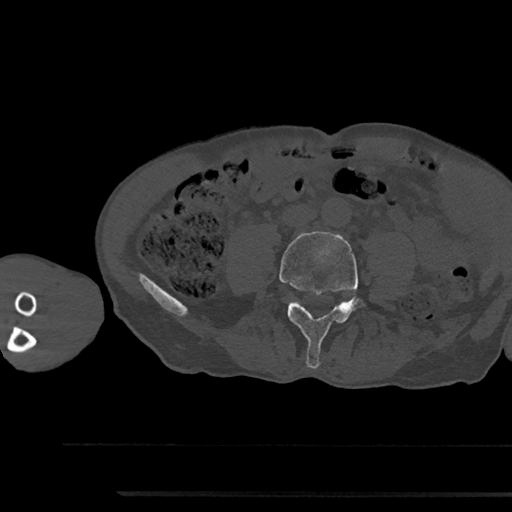
CT including the spine, one axial slice; position 405 of 797 along the scan axis; reconstruction kernel Br40s/3; 120 kVp; bone window (W 1800 / L 400 HU); 0.5 mm slice thickness; 512 × 512 image matrix. Male patient, age 79 years. From the clinical record (not read from this slice): primary cancer: prostate.
Outlined on this slice (semi-automatically segmented with operator editing):
- L4 vertebra: bounding box (x1, y1, x2, y2) in pixels: (279, 231, 360, 369)